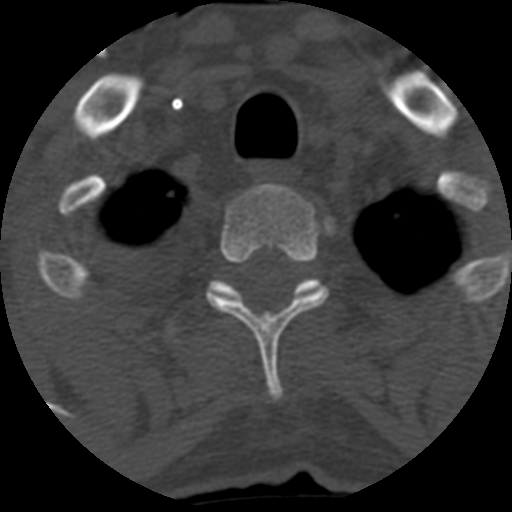
CT including the spine, one axial slice. Slice 501 of 708 in the series (ordered by position). 120 kVp. One of 3 acquisitions stored at this slice position. Bone window (W 1800 / L 400 HU). 1.25 mm slice thickness. 512 × 512 image matrix, field of view 160 × 160 mm. Patient age 55 years. From the clinical record (not read from this slice): primary cancer: colon; vertebrae with lytic lesions (as recorded): T12, L1, L5.
Annotated regions visible in this slice (semi-automatically segmented with operator editing):
- T2 vertebra: box from (x=208, y=183) to (x=329, y=402) px
- T3 vertebra: (x=165, y=280)–(x=319, y=339)